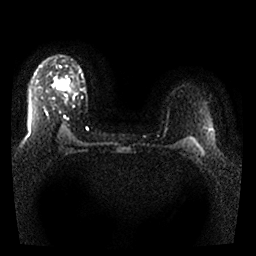
Breast MRI, one axial slice; slice 23 of 25 in the series (ordered by position); diffusion-weighted series; image 2 of 4 stored at this slice position (different b-values; order by instance number); 1.5 T; 4 mm slice thickness; 256 × 256 image matrix. Female patient.
Structures marked on this image (outlined manually by an expert reader):
- tumour on diffusion-weighted imaging: bounding box (x1, y1, x2, y2) in pixels: (55, 79, 60, 88)